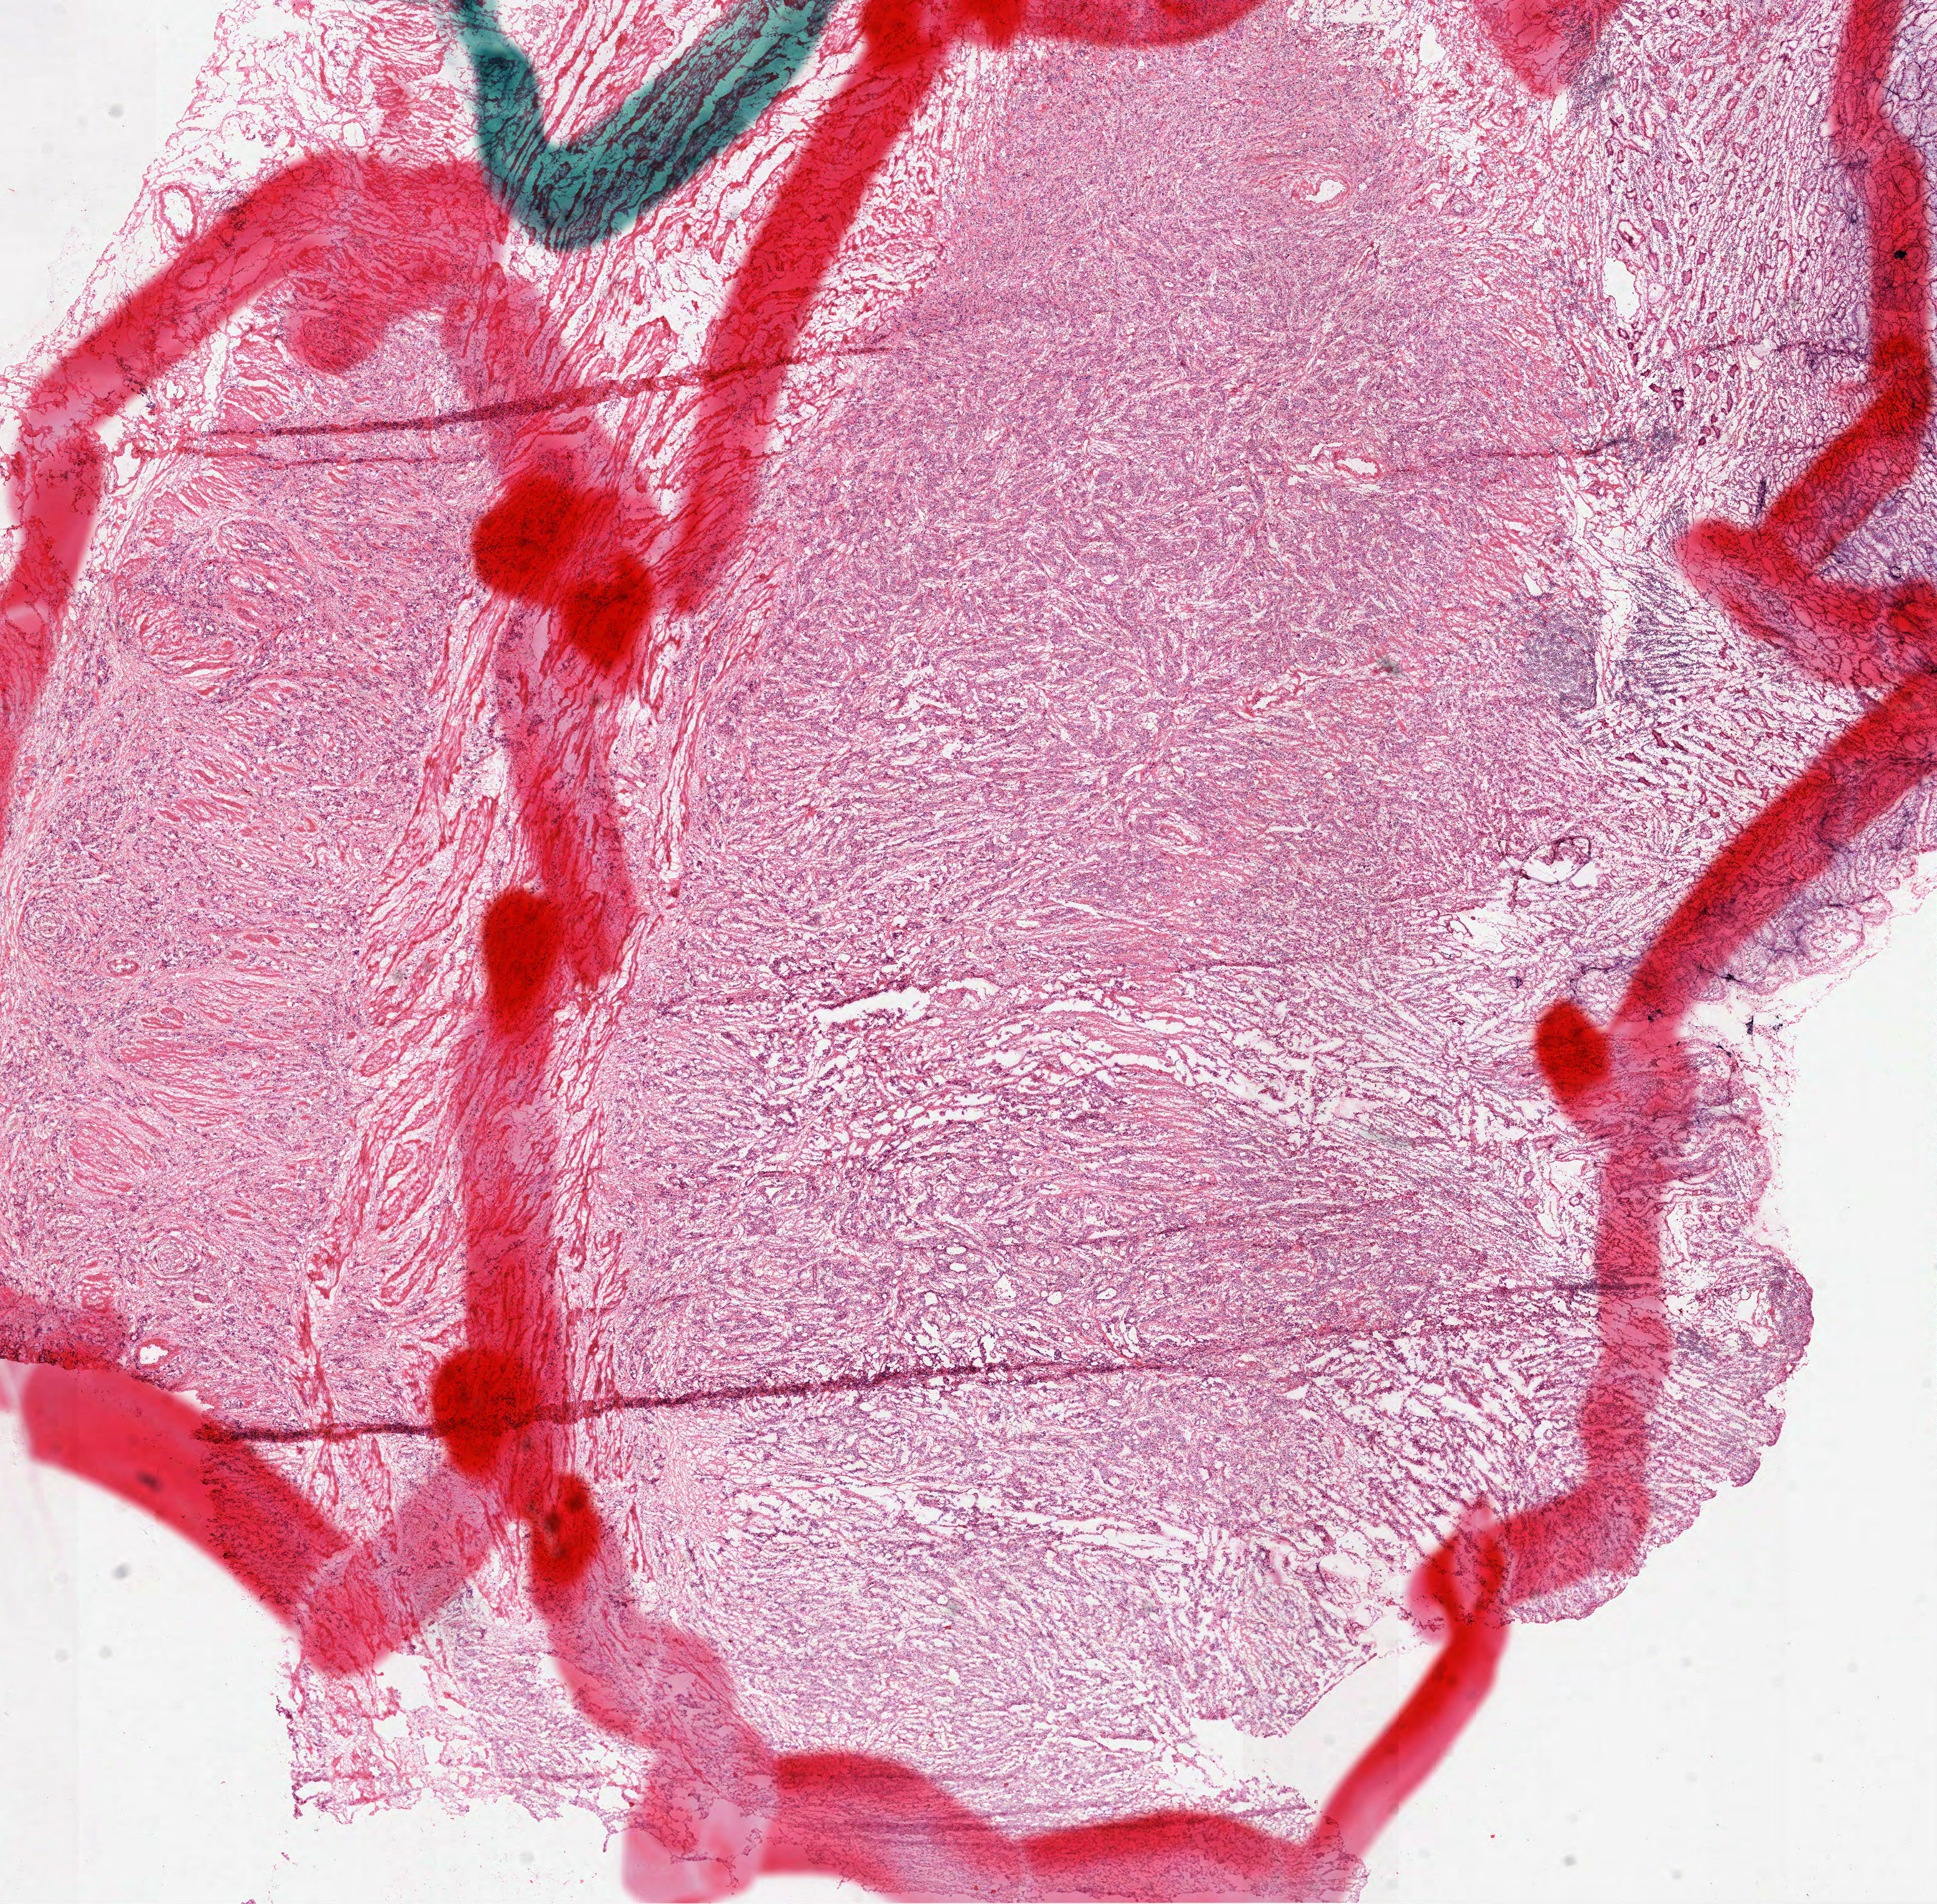
Whole-slide histology image, Hematoxylin and eosin (H&E) stained — a low-resolution overview of the entire scanned area, about 12.5 x 12.3 mm (from a 40x scan); frozen section; primary tumour sample from the stomach. Patient: female, age at initial diagnosis 74 years. Histologic grade: G2 (moderately differentiated). Slide review estimates, as recorded: tumour cells 100%, tumour nuclei 75%, normal cells 0%, stromal cells 0%, necrosis 0%. Inflammatory infiltration, as recorded: lymphocyte infiltration 10%, monocyte infiltration 0%, neutrophil infiltration 0%.
* histologic diagnosis: Adenocarcinoma, NOS (body of stomach)
* AJCC pathologic stage: IIB (7th edition)
* lymph nodes positive (case pathology): 2 of 4 examined